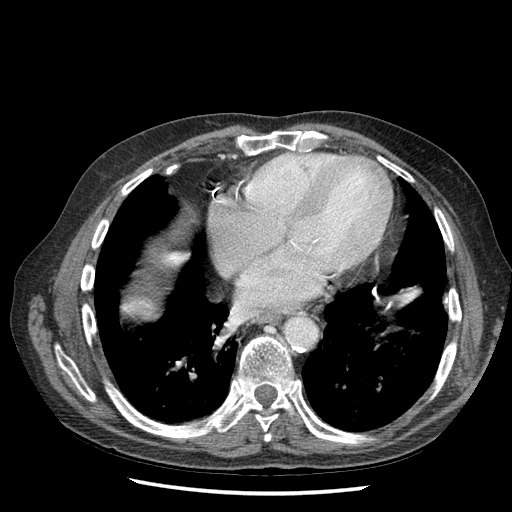
Contrast-enhanced abdominal CT (liver protocol), one axial slice; slice 64 of 67 in the series (ordered by position); 120 kVp; soft-tissue window (W 400 / L 40 HU); 2.5 mm slice thickness; 512 × 512 image matrix, field of view 360 × 360 mm. Case-level facts recorded for this patient, not image findings: diagnosis: hepatocellular carcinoma (patient treated with transarterial chemoembolisation; whether this scan precedes or follows treatment is not stated here); TNM stage (as recorded): Stage-I; Child-Pugh class: A; tumour nodularity: uninodular.
Annotated regions visible in this slice (semi-automatic segmentation, software-assisted and operator-edited):
- liver parenchyma outside the tumour (the mass and vessels are separate outlines, so this box may not span the whole liver): bounding box <142,302,150,313> (left, top, right, bottom; pixels)
- liver vessels: <145,303,150,308>